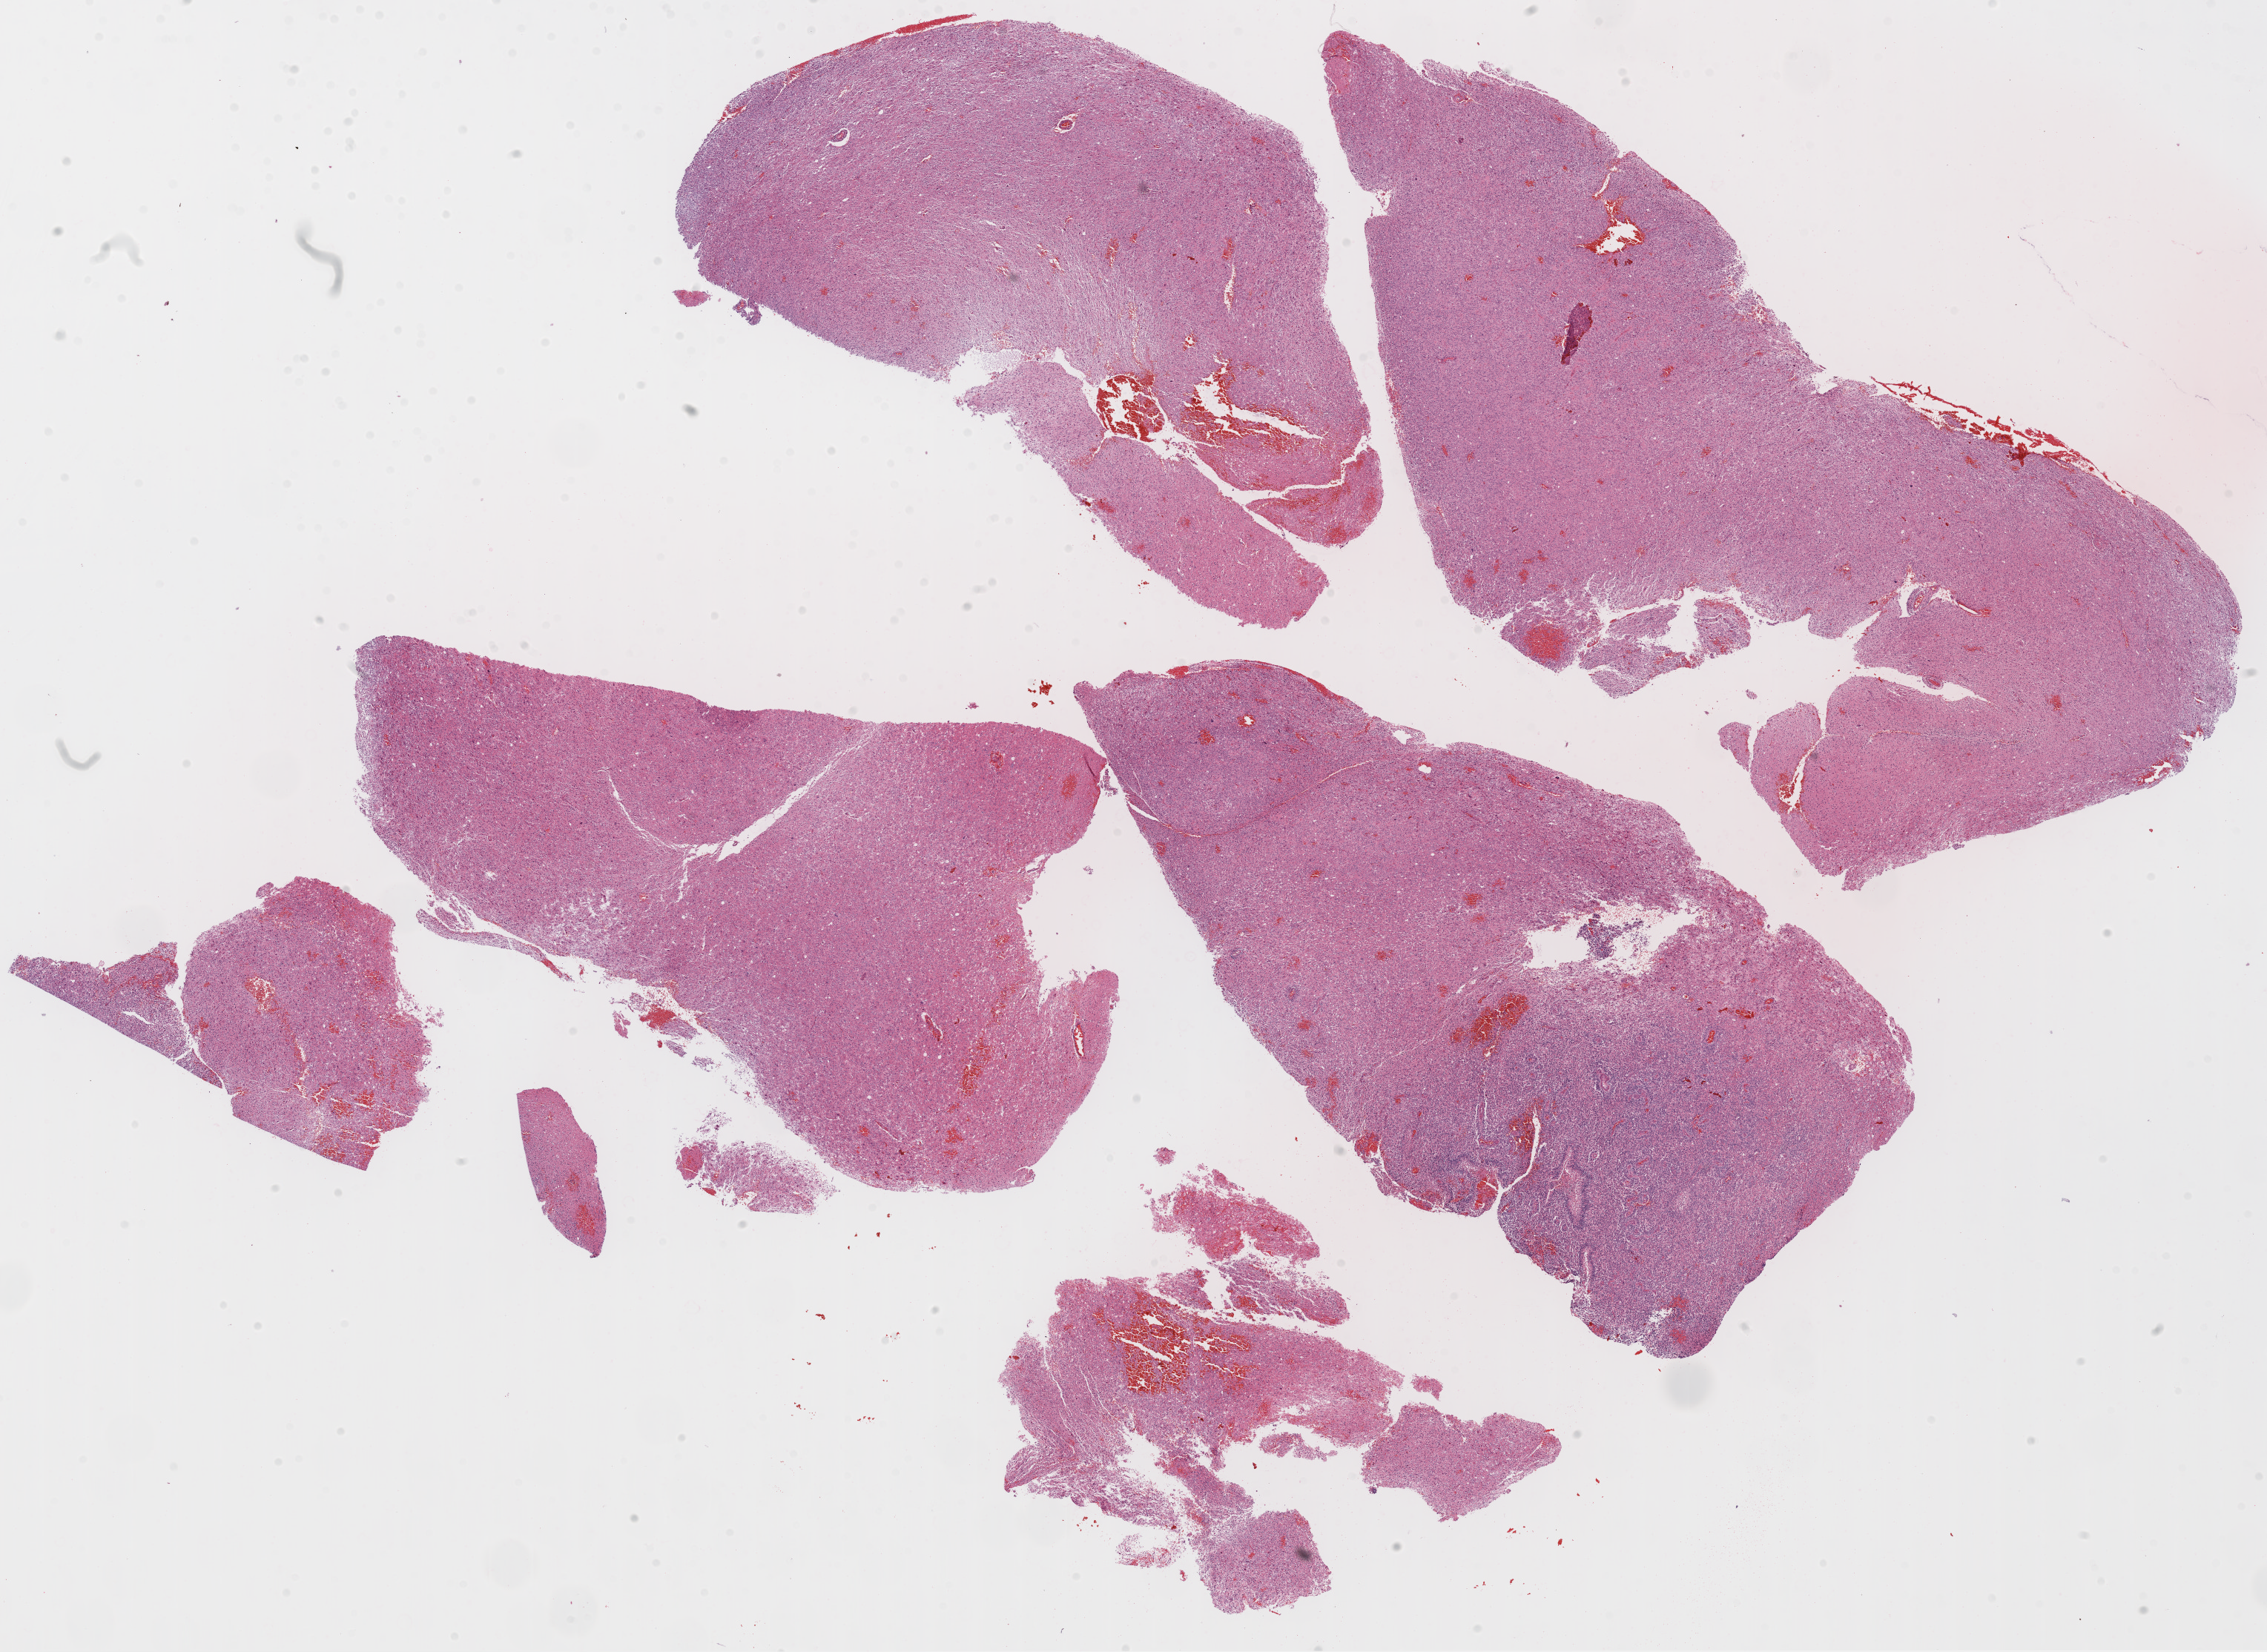
Whole-slide histology image, H&E-stained, whole scanned area (about 24.7 x 18.0 mm, acquisition: 20x scan) shown as a low-resolution overview. FFPE section. Sample: primary tumour, brain. Male patient; age at initial diagnosis 51 years.
Histologic diagnosis: Glioblastoma.